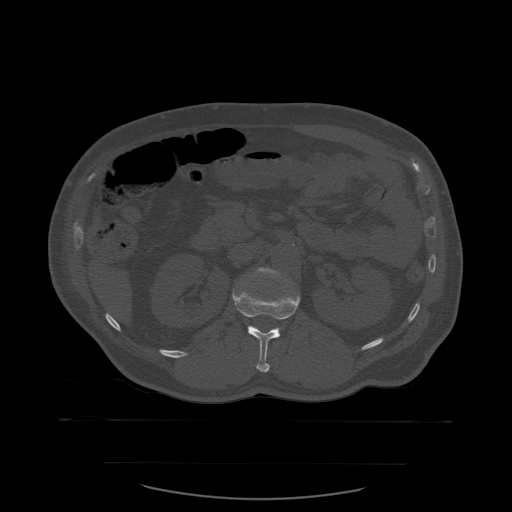
CT including the spine, one axial slice. Slice 241 of 590 in the series (ordered by position). Bone window (W 1800 / L 400 HU). 512 × 512 image matrix. Patient age 71 years. Case-level facts recorded for this patient, not image findings: primary cancer: lung; vertebrae with lytic lesions (as recorded): T1, T2, L5, S1.
Structures marked on this image (semi-automatic segmentation, software-assisted and operator-edited):
- L1 vertebra: box from (x=232, y=274) to (x=301, y=373) px
- L2 vertebra: (x=244, y=268)–(x=281, y=285)